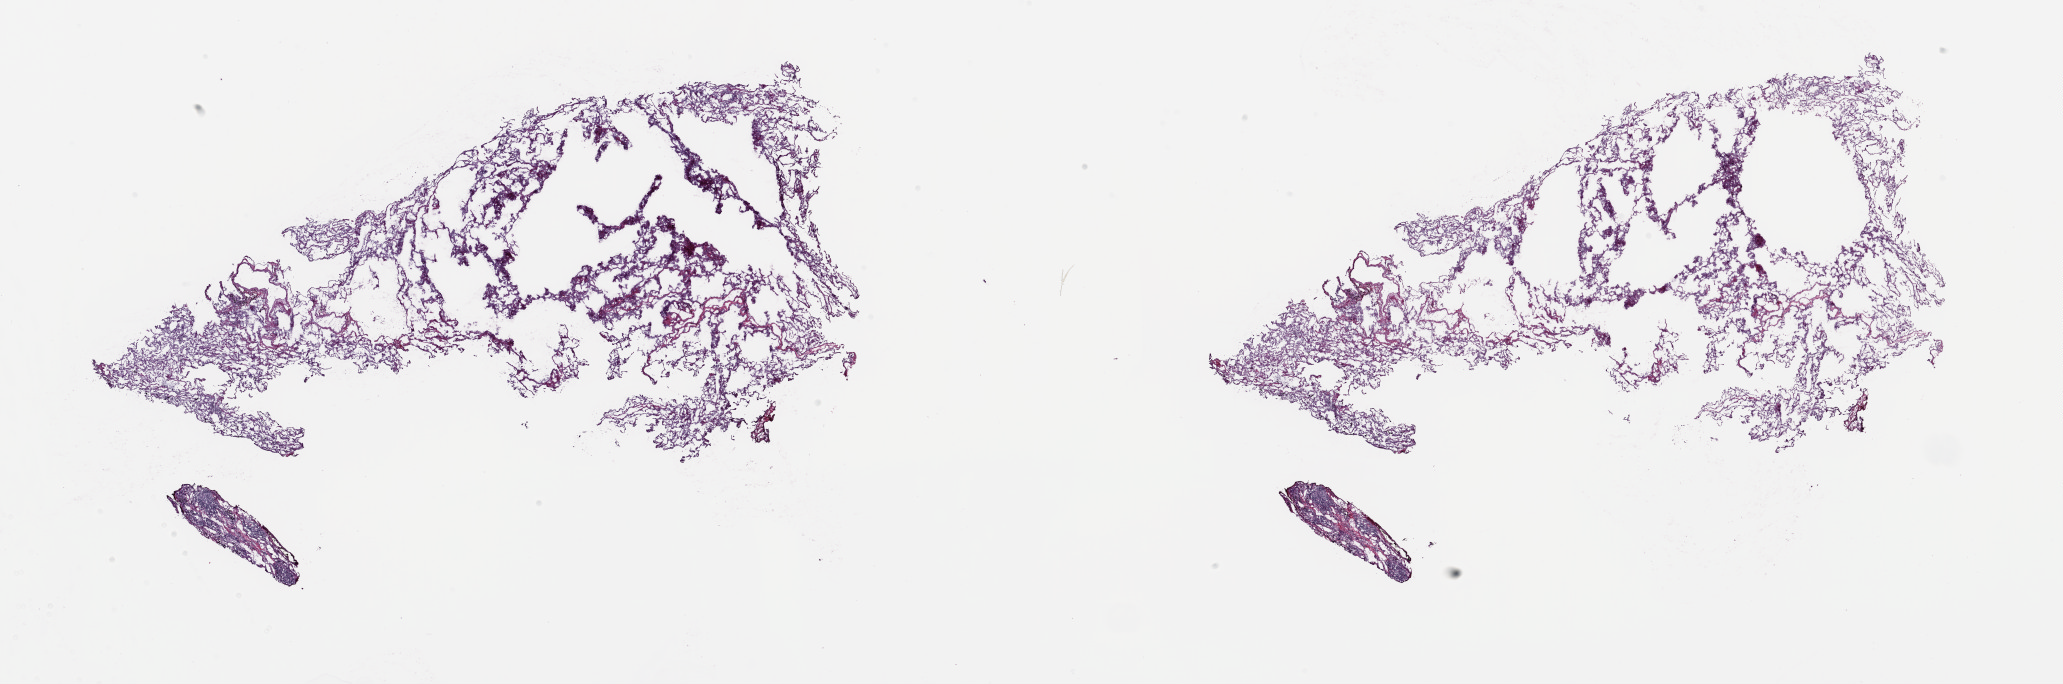
Digitized H&E-stained tissue section (whole slide) — a low-resolution overview of the entire scanned area, about 32.7 x 10.9 mm (slide scanned at 20x), frozen section from the top of the tissue portion, lung, solid tissue normal (non-tumour tissue) sample. Male, age 61 years at initial diagnosis. Composition of this section per pathologist review: tumour cells 0%, tumour nuclei 0%.
This section: solid tissue normal (non-tumour) sample from the same patient. Patient diagnosis: Adenocarcinoma, NOS.